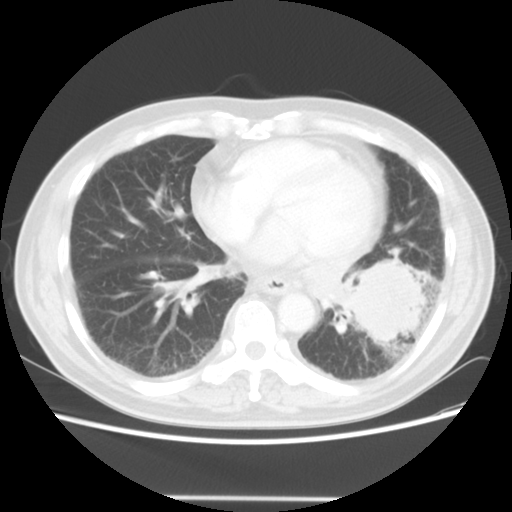
Chest CT, one axial slice; slice 18 of 56 in the series (ordered by position); reconstruction kernel STANDARD; 140 kVp; lung window (W 1500 / L -600 HU); 5 mm slice thickness; 512 × 512 image matrix, field of view 360 × 360 mm. Male patient, age 66 years. Case-level facts recorded for this patient, not image findings: clinical TNM (as recorded): T4 N3 M0; histopathological grade: G3.
Annotated regions visible in this slice (bounding box drawn by a radiologist):
- lung tumour (recorded histology: small cell carcinoma): box from (x=335, y=227) to (x=431, y=357) px